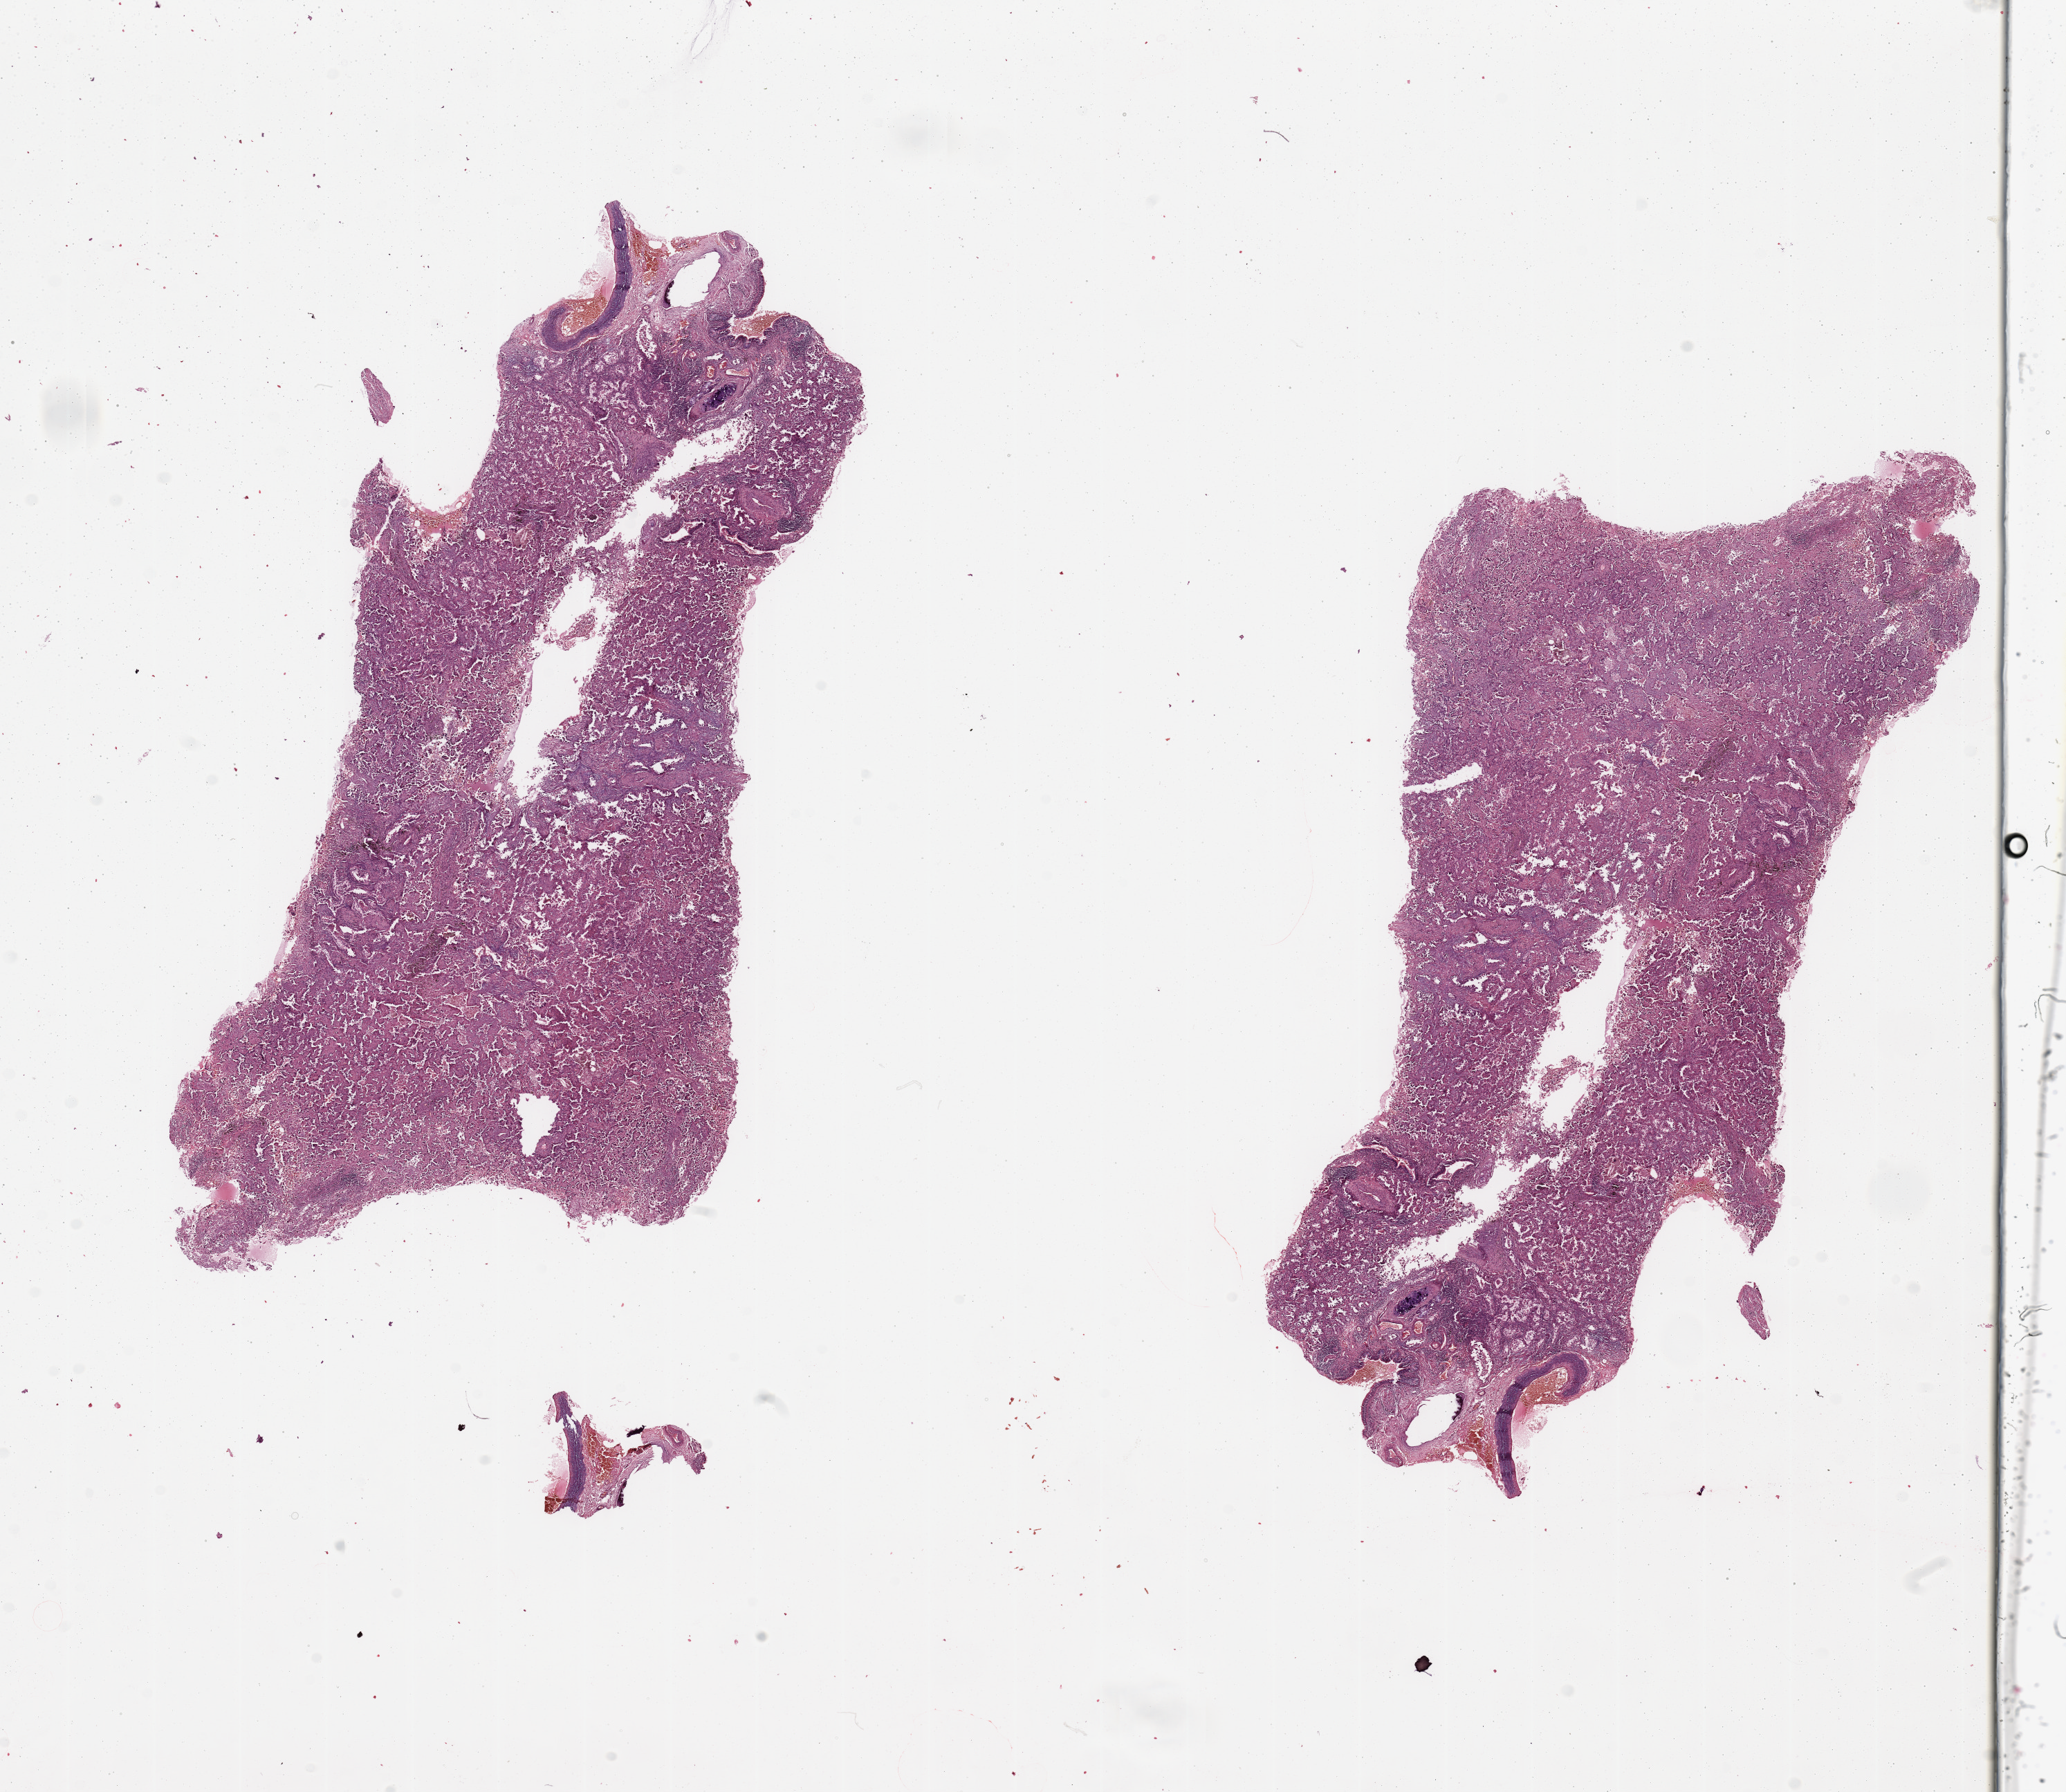
H&E-stained whole-slide image, low-resolution overview of the scanned area, about 23.6 x 20.5 mm (acquisition: 20x scan). Lung, tumour tissue. 73-year-old female patient. Histologic grade: G2 (moderately differentiated).
Histologic diagnosis: Adenocarcinoma, NOS. Primary tumour site (as recorded): right upper lobe. AJCC pathologic stage: IB.